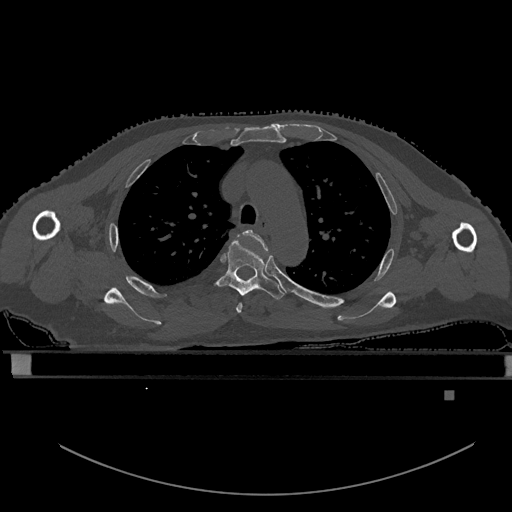
CT including the spine, one axial slice. Position 414 of 969 along the scan axis. Bone window (W 1800 / L 400 HU). 0.5 mm slice thickness. 512 × 512 image matrix, field of view 456 × 456 mm. Patient: male, 82 years. Case-level facts recorded for this patient, not image findings: primary cancer: prostate; vertebrae with lytic lesions (as recorded): T11, T9, T8, T2.
Structures marked on this image (semi-automatically segmented with operator editing):
- T3 vertebra: box from (x=236, y=229) to (x=268, y=313) px
- T4 vertebra: (x=216, y=238)–(x=285, y=299)